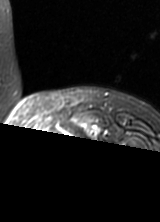
MRI of an extremity soft-tissue mass, one axial slice; T2-weighted fat-saturated; MR volume resampled by the dataset authors to the PET/CT grid (not the native acquisition matrix); 160 × 222 image matrix, field of view 156 × 217 mm. Female patient. Case-level facts recorded for this patient, not image findings: histological type: pleomorphic leiomyosarcoma; grade: high; site of the primary tumour: left thigh.
Annotated regions visible in this slice (expert contour drawn on MRI and transferred to this co-registered scan by the dataset authors):
- gross tumour volume including surrounding oedema: bounding box <32,132,53,149> (left, top, right, bottom; pixels)